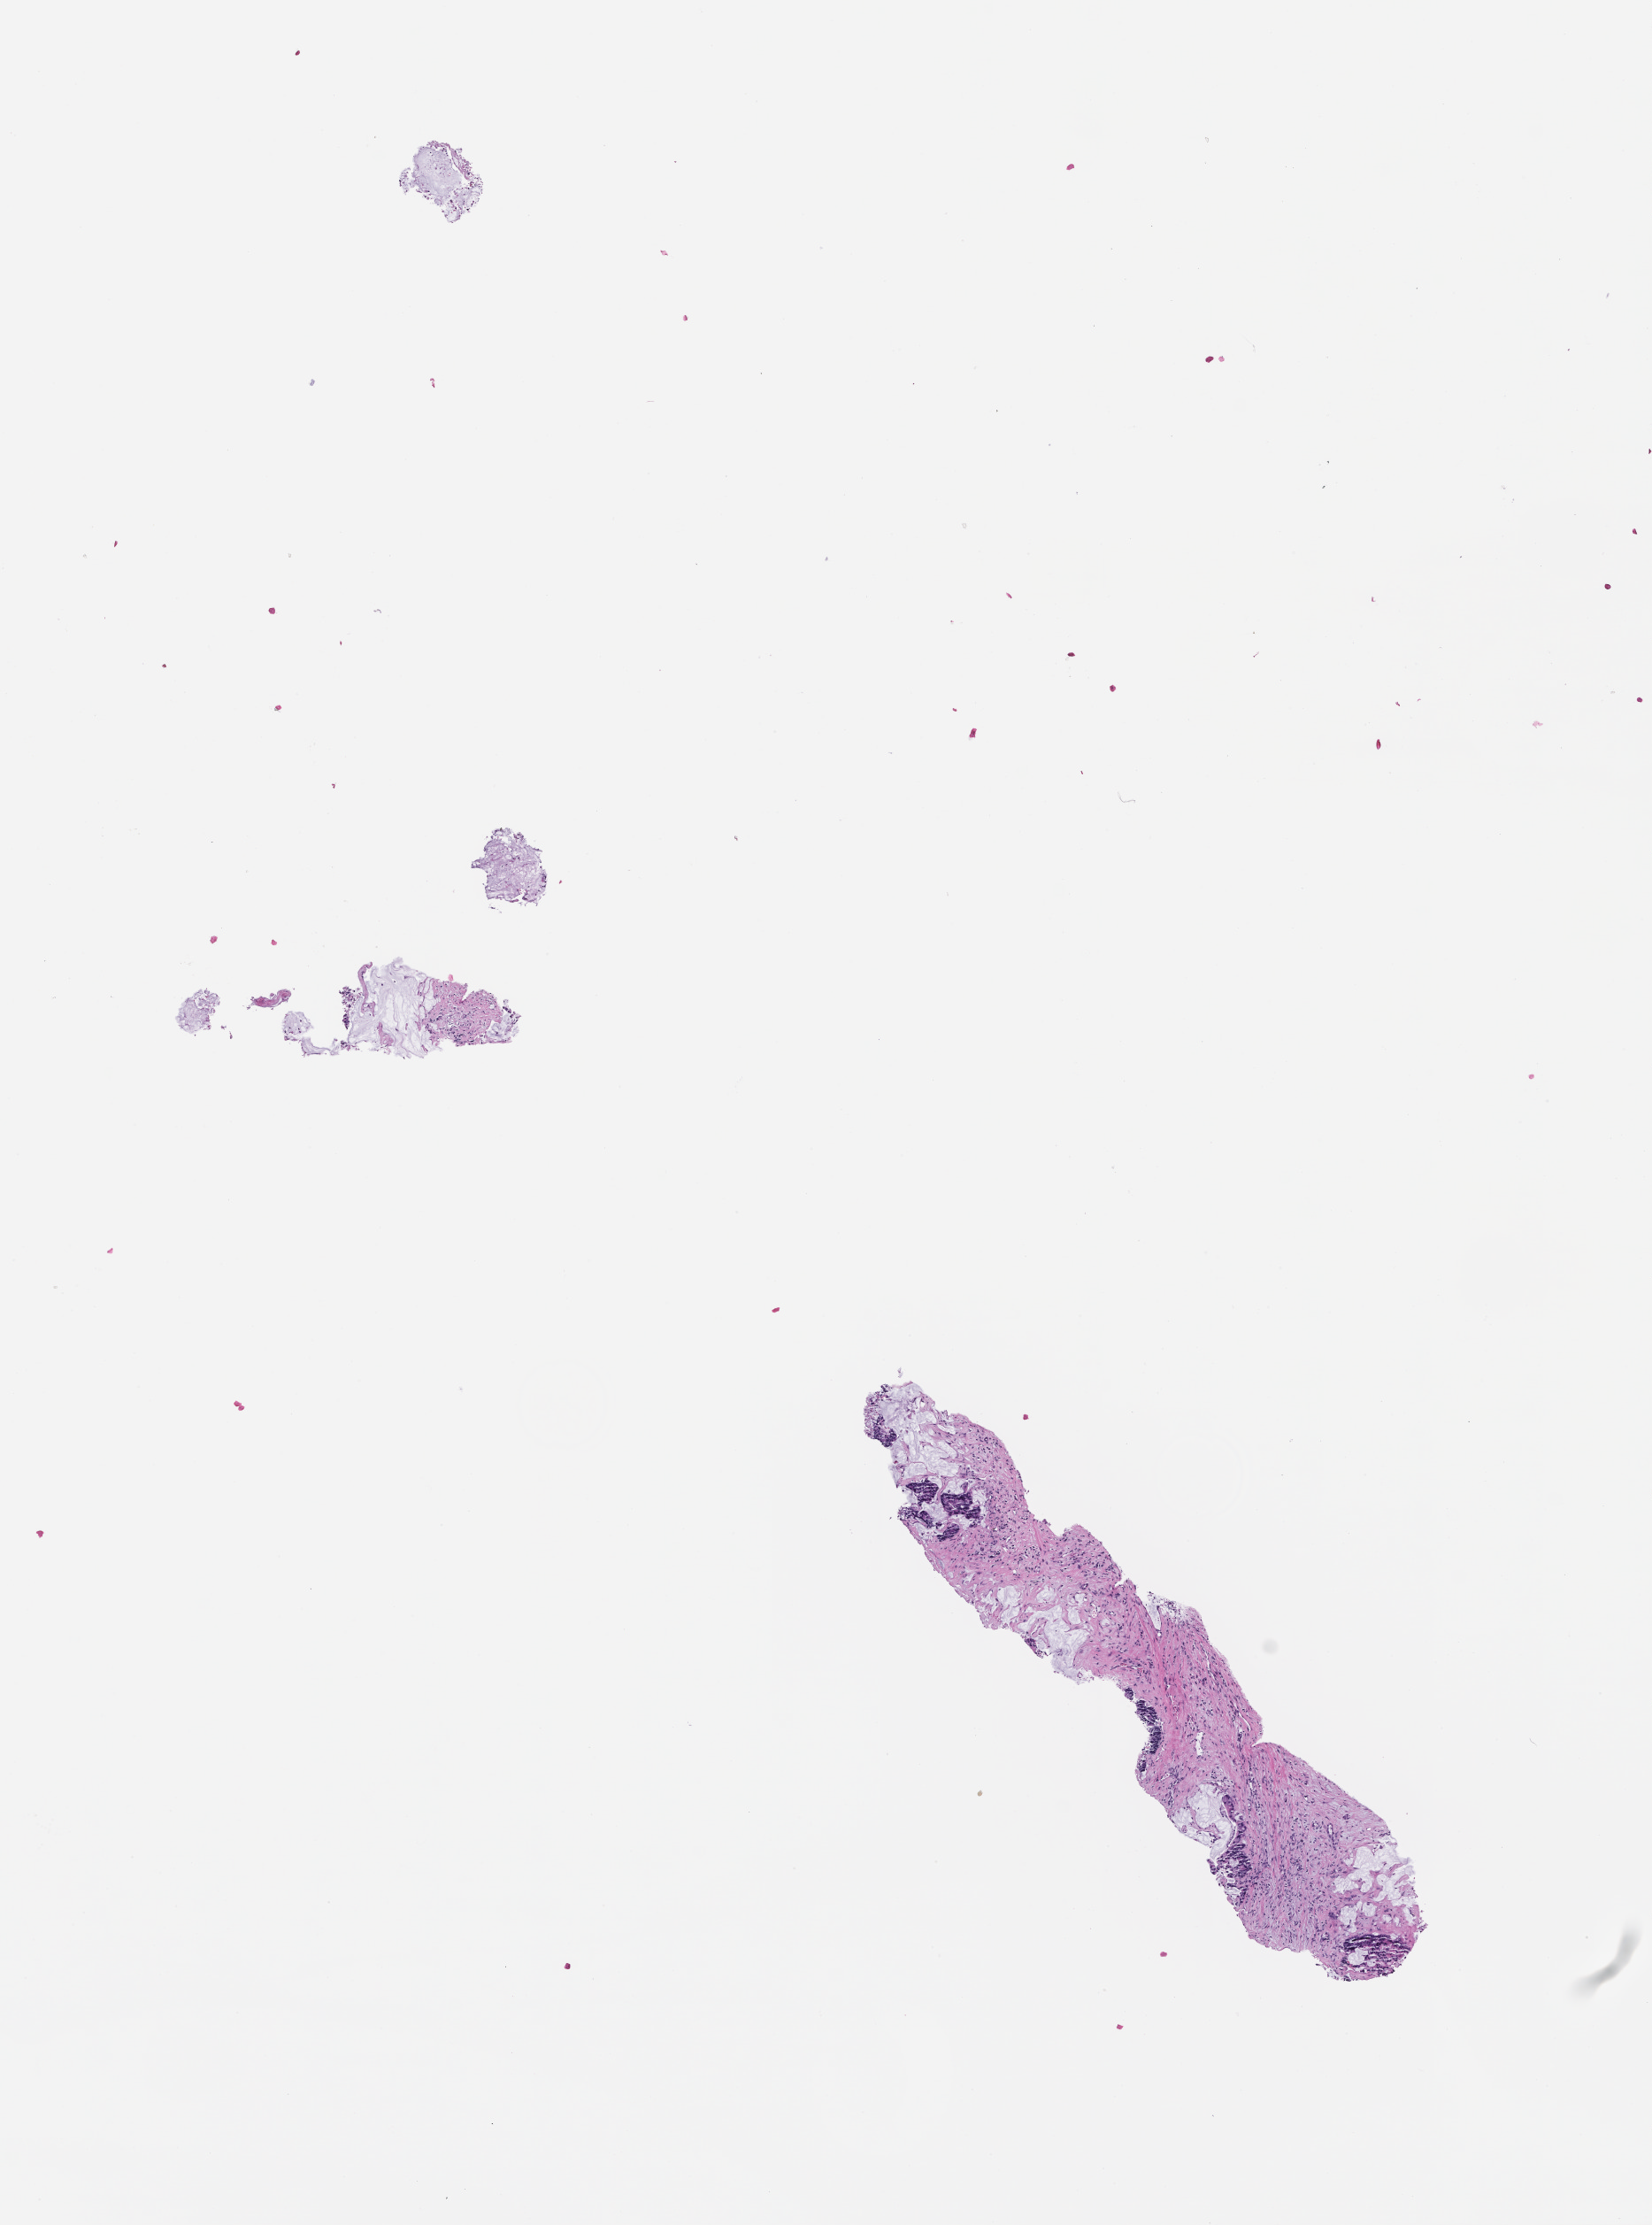
Digitized H&E-stained section, low-resolution overview of the scanned area, about 7.5 x 10.2 mm; FFPE section; collected at baseline (before treatment). Patient sex: male.
This section: metastasis (sampled organ not recorded). Patient diagnosis (primary): Colorectal Carcinoma.